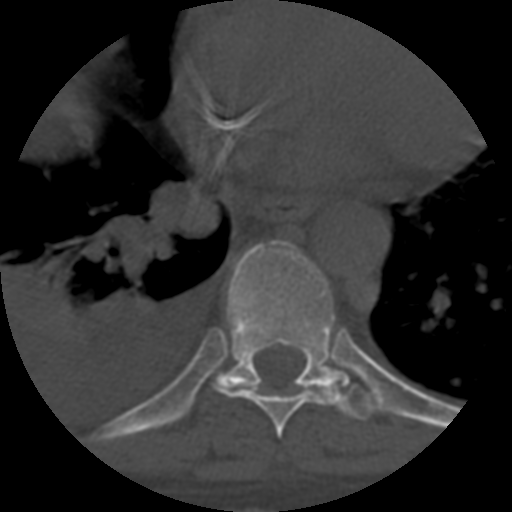
CT including the spine, one axial slice; position 386 of 708 along the scan axis; reconstruction kernel STANDARD; one of 3 acquisitions stored at this slice position; bone window (W 1800 / L 400 HU); 1.25 mm slice thickness; 512 × 512 image matrix, field of view 160 × 160 mm. Patient age 55 years. Case-level facts recorded for this patient, not image findings: primary cancer: colon.
Outlined on this slice (semi-automatically segmented with operator editing):
- T8 vertebra: box from (x=213, y=380) to (x=339, y=438) px
- T9 vertebra: (x=216, y=244)–(x=374, y=421)